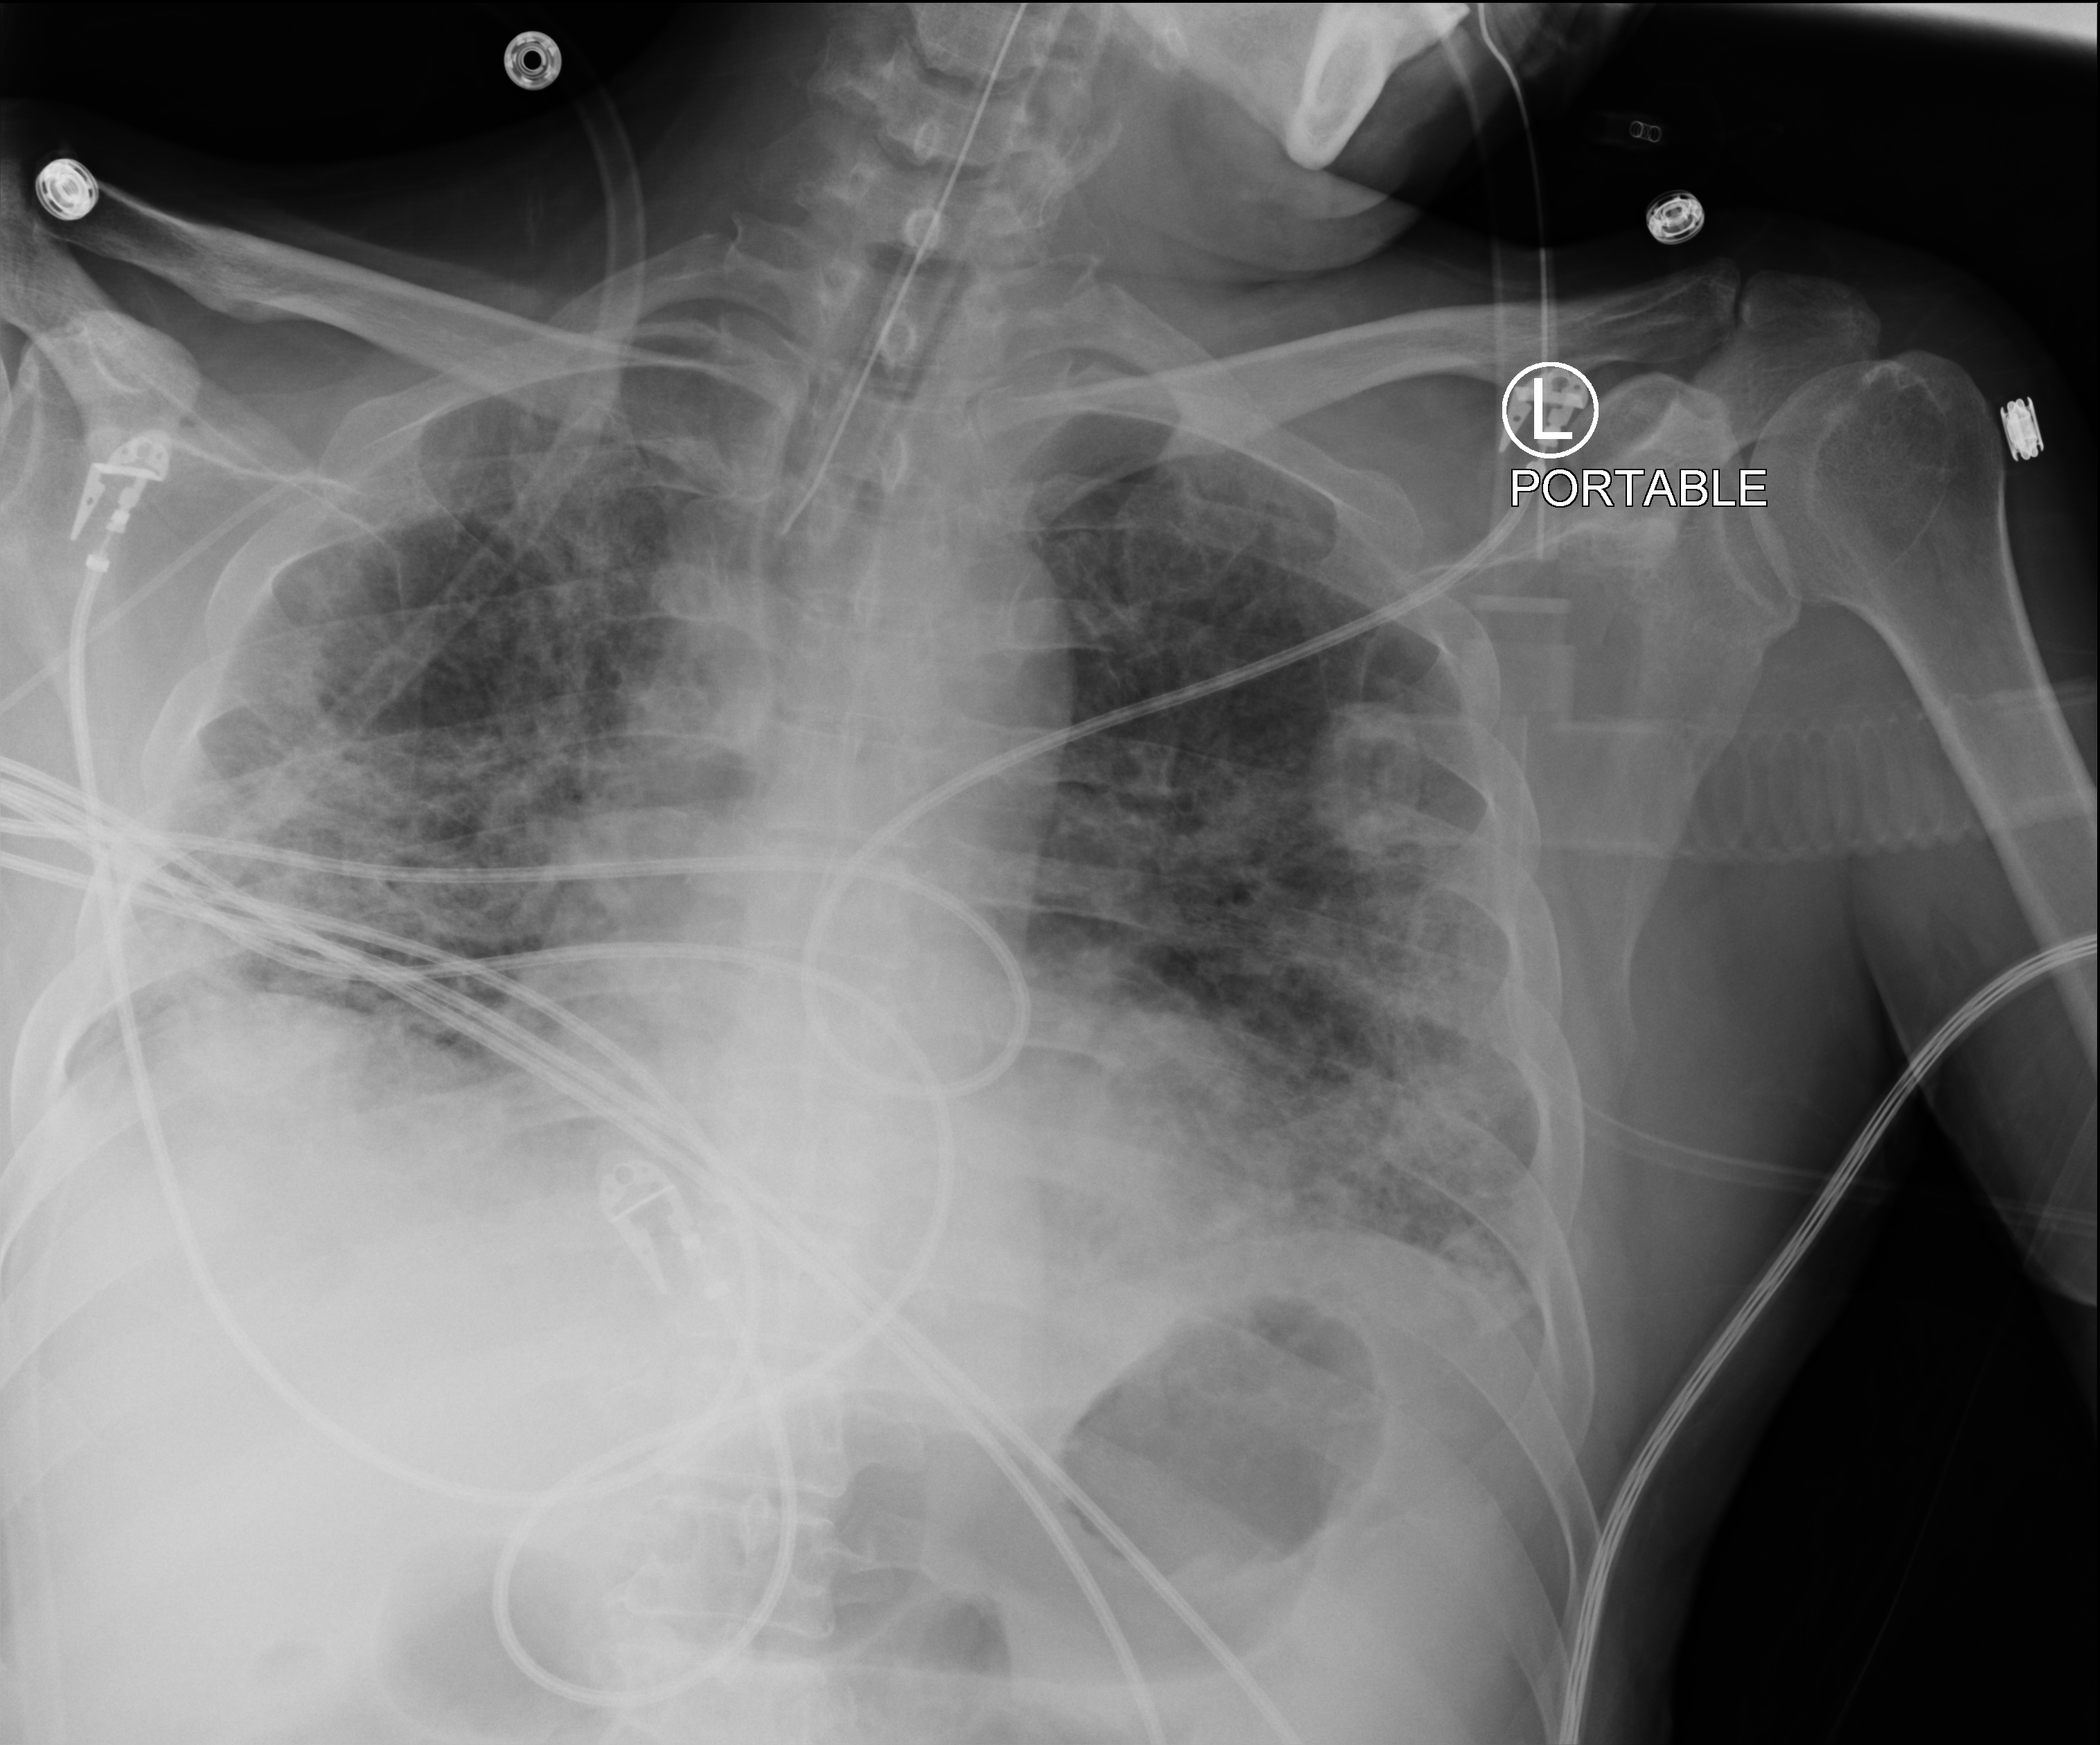
Portable chest radiograph, anteroposterior (AP) projection. Male patient hospitalised with COVID-19, age 18–59 years.
Admission-level facts for this patient (not findings on this image; timing relative to this image not recorded): admitted to intensive care during this hospital stay: yes; mechanically ventilated during this hospital stay: yes; COPD (admission record): no.